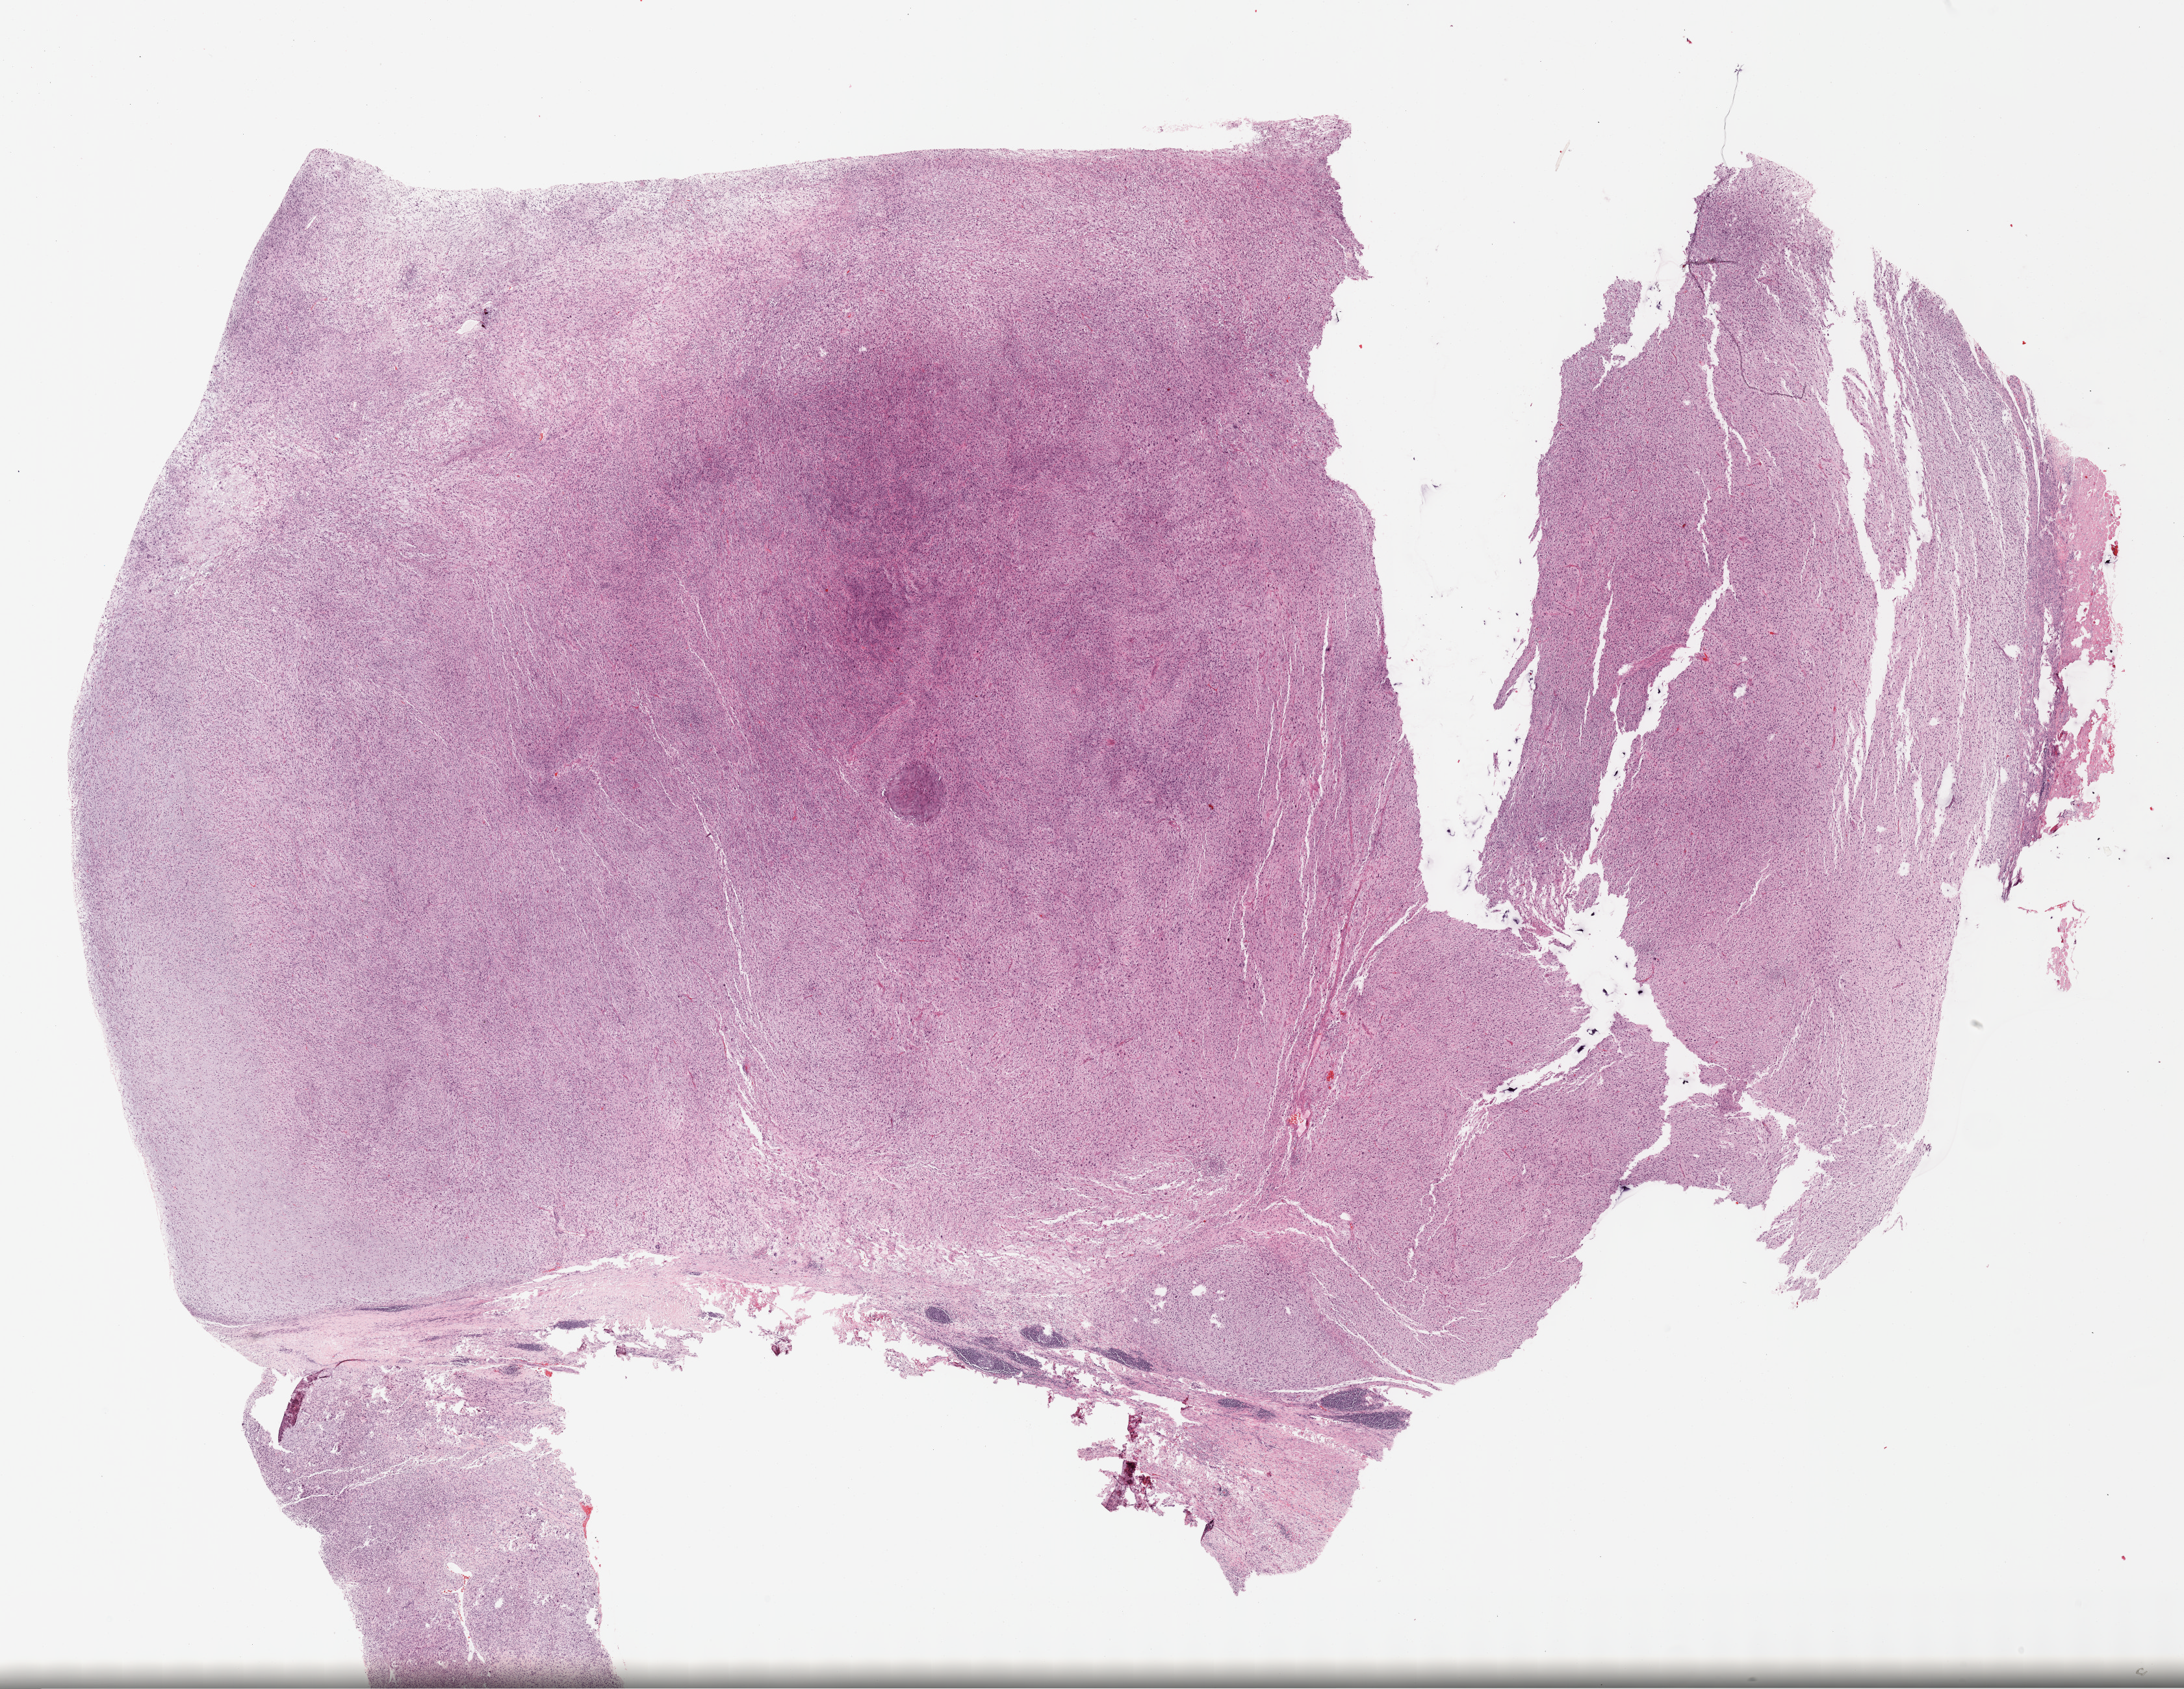
Hematoxylin and eosin (H&E) stained whole-slide image — a low-resolution overview of the entire scanned area, about 27.2 x 21.0 mm (slide scanned at 40x); FFPE section; connective, subcutaneous and other soft tissues, primary tumour sample. Patient: female, age at initial diagnosis 61 years.
* histologic diagnosis: Undifferentiated sarcoma (connective, subcutaneous and other soft tissues of lower limb and hip)